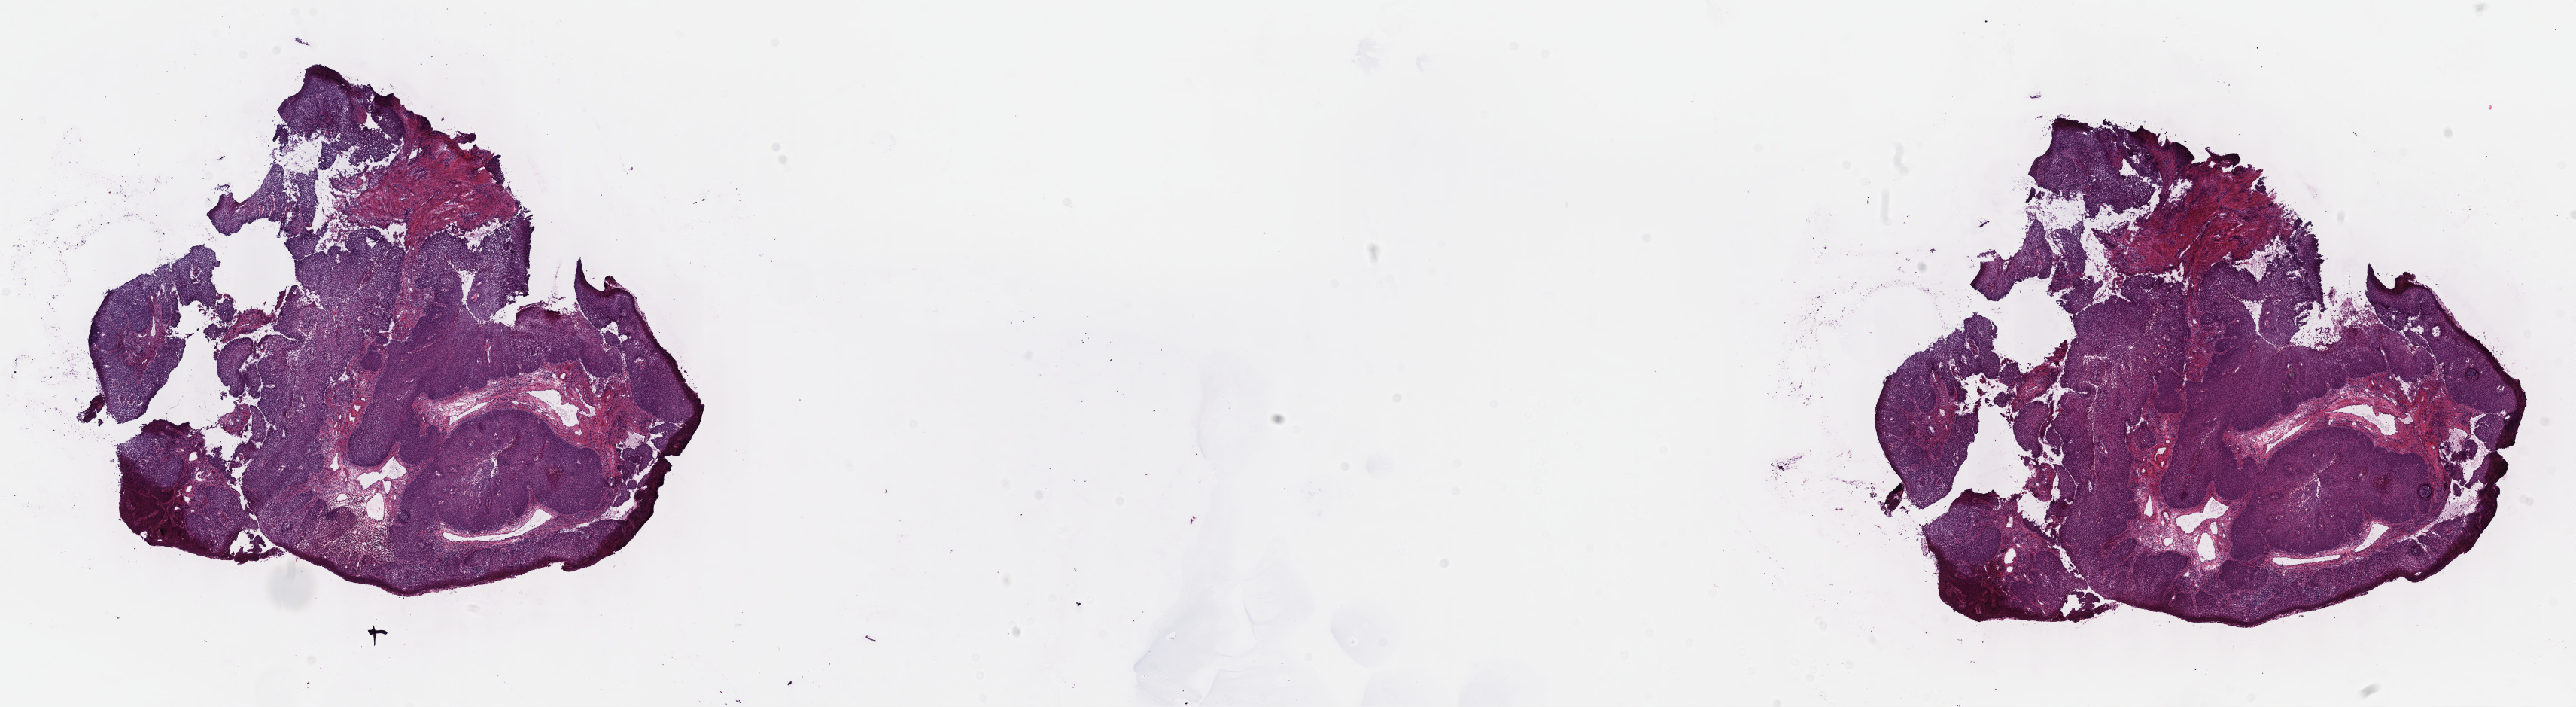
Whole-slide histology image, H&E — a low-resolution overview of the entire scanned area, about 27.7 x 7.6 mm (acquisition: 40x scan), frozen section from the top of the tissue portion, cervix, primary tumour sample. Female, age 36 years at initial diagnosis. Histologic grade: GX (grade cannot be assessed). Composition of this section per pathologist review: tumour cells 80%, tumour nuclei 80%, normal cells 20%, stromal cells 0%, necrosis 0%. Infiltration values recorded for this section: lymphocyte infiltration 5%, monocyte infiltration 0%, neutrophil infiltration 0%.
Pathologic diagnosis: Squamous cell carcinoma, NOS (cervix uteri). FIGO stage: IB1.